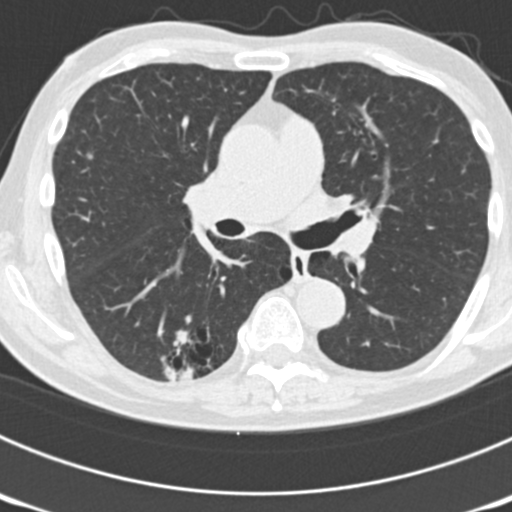
Chest CT (low-dose screening protocol), one axial image; third screening round (two years after baseline); lung window (W 1500 / L -600 HU); 2 mm slice thickness; 120 kVp. Male participant, aged 70 years at enrolment. Current smoker at enrolment.
• Expert-annotated lung lesion, box from (x=144, y=308) to (x=236, y=385) px.
• The screening reader recorded 3 non-calcified nodules or masses ≥4 mm on this exam (right upper lobe, left upper lobe, right lower lobe); which of them this box marks is not recorded.
• Participant outcome: lung cancer diagnosed 14 days after this screen — bronchiolo-alveolar adenocarcinoma, NOS, right lower lobe, poorly differentiated (G3), stage IB (AJCC 6th edition), 30 mm at pathology.